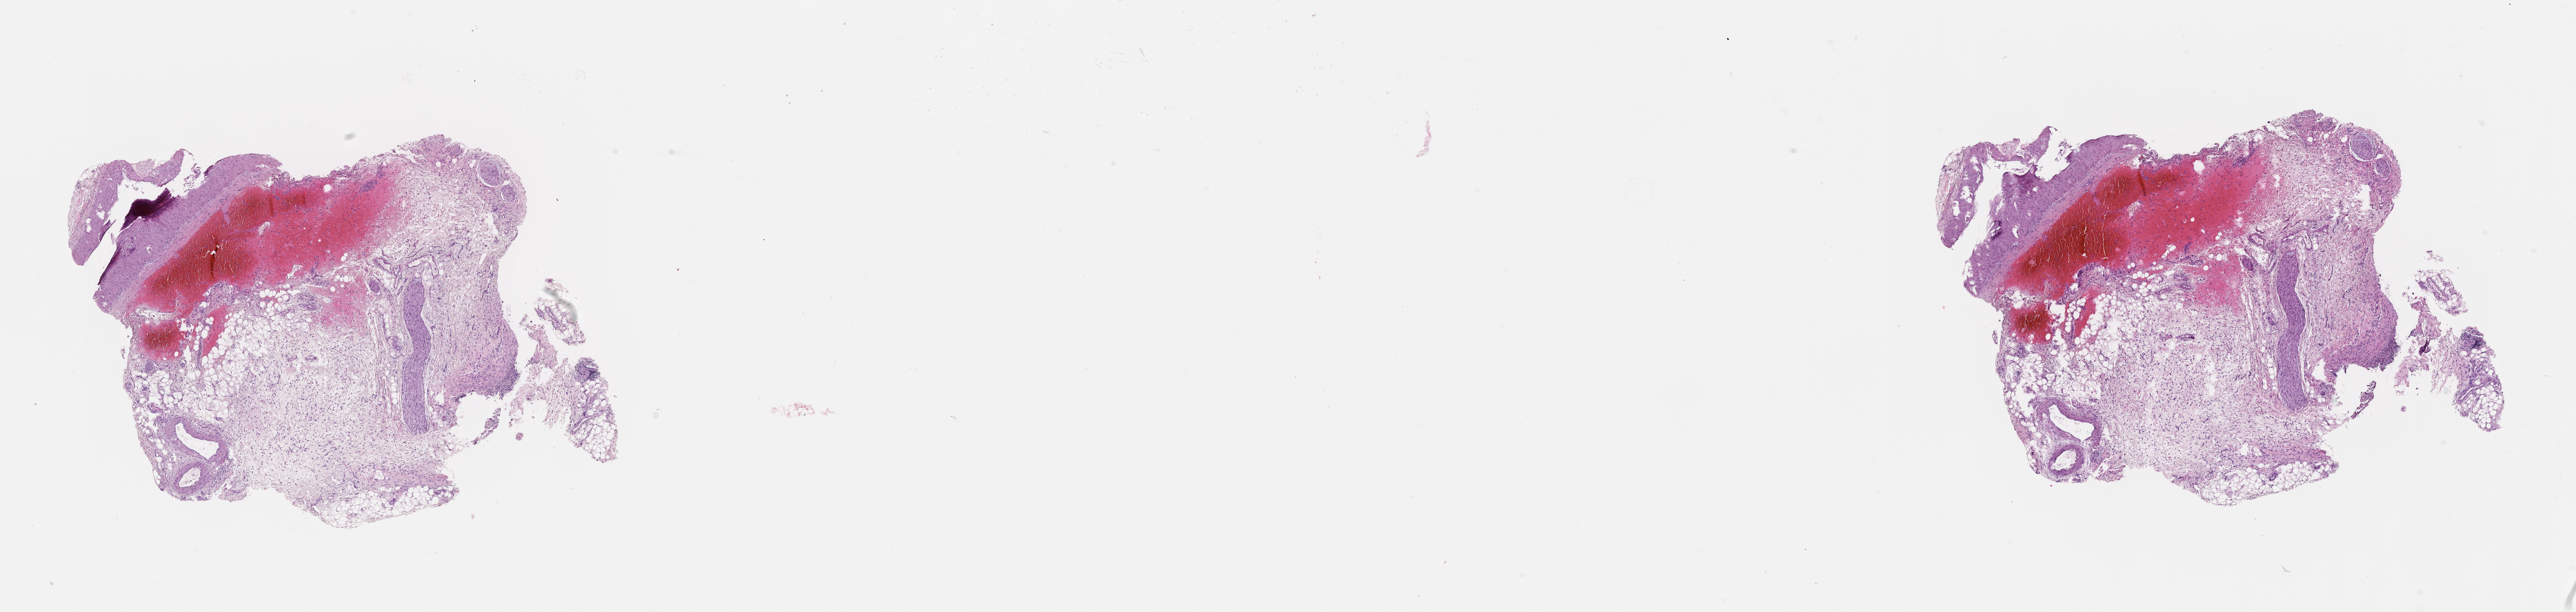
H&E-stained whole-slide image, whole scanned area (about 30.1 x 7.1 mm, acquisition: 20x scan) shown as a low-resolution overview. Pancreas, tumour tissue. 69-year-old male patient. Histologic grade: G2 (moderately differentiated).
- AJCC pathologic stage: IA
- primary tumour site (as recorded): head
- diagnosis: Infiltrating duct carcinoma, NOS